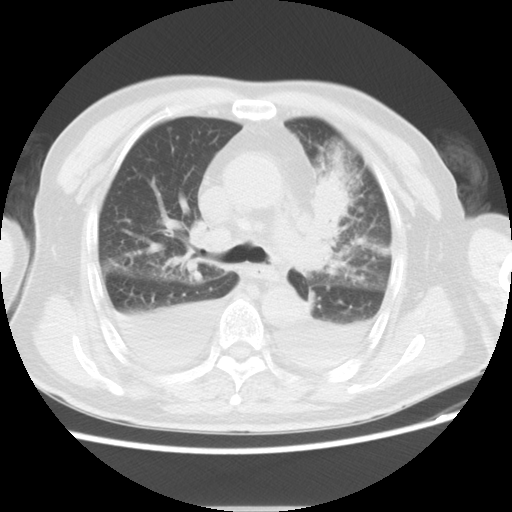
Chest CT, one axial slice. 120 kVp. Lung window (W 1500 / L -600 HU). 512 × 512 image matrix, field of view 350 × 350 mm. Male patient, age 66 years. Case-level facts recorded for this patient, not image findings: clinical TNM (as recorded): T1c N0 M0.
Structures marked on this image (bounding box drawn by a radiologist):
- lung tumour (recorded histology: adenocarcinoma): bounding box <315,171,351,233> (left, top, right, bottom; pixels)